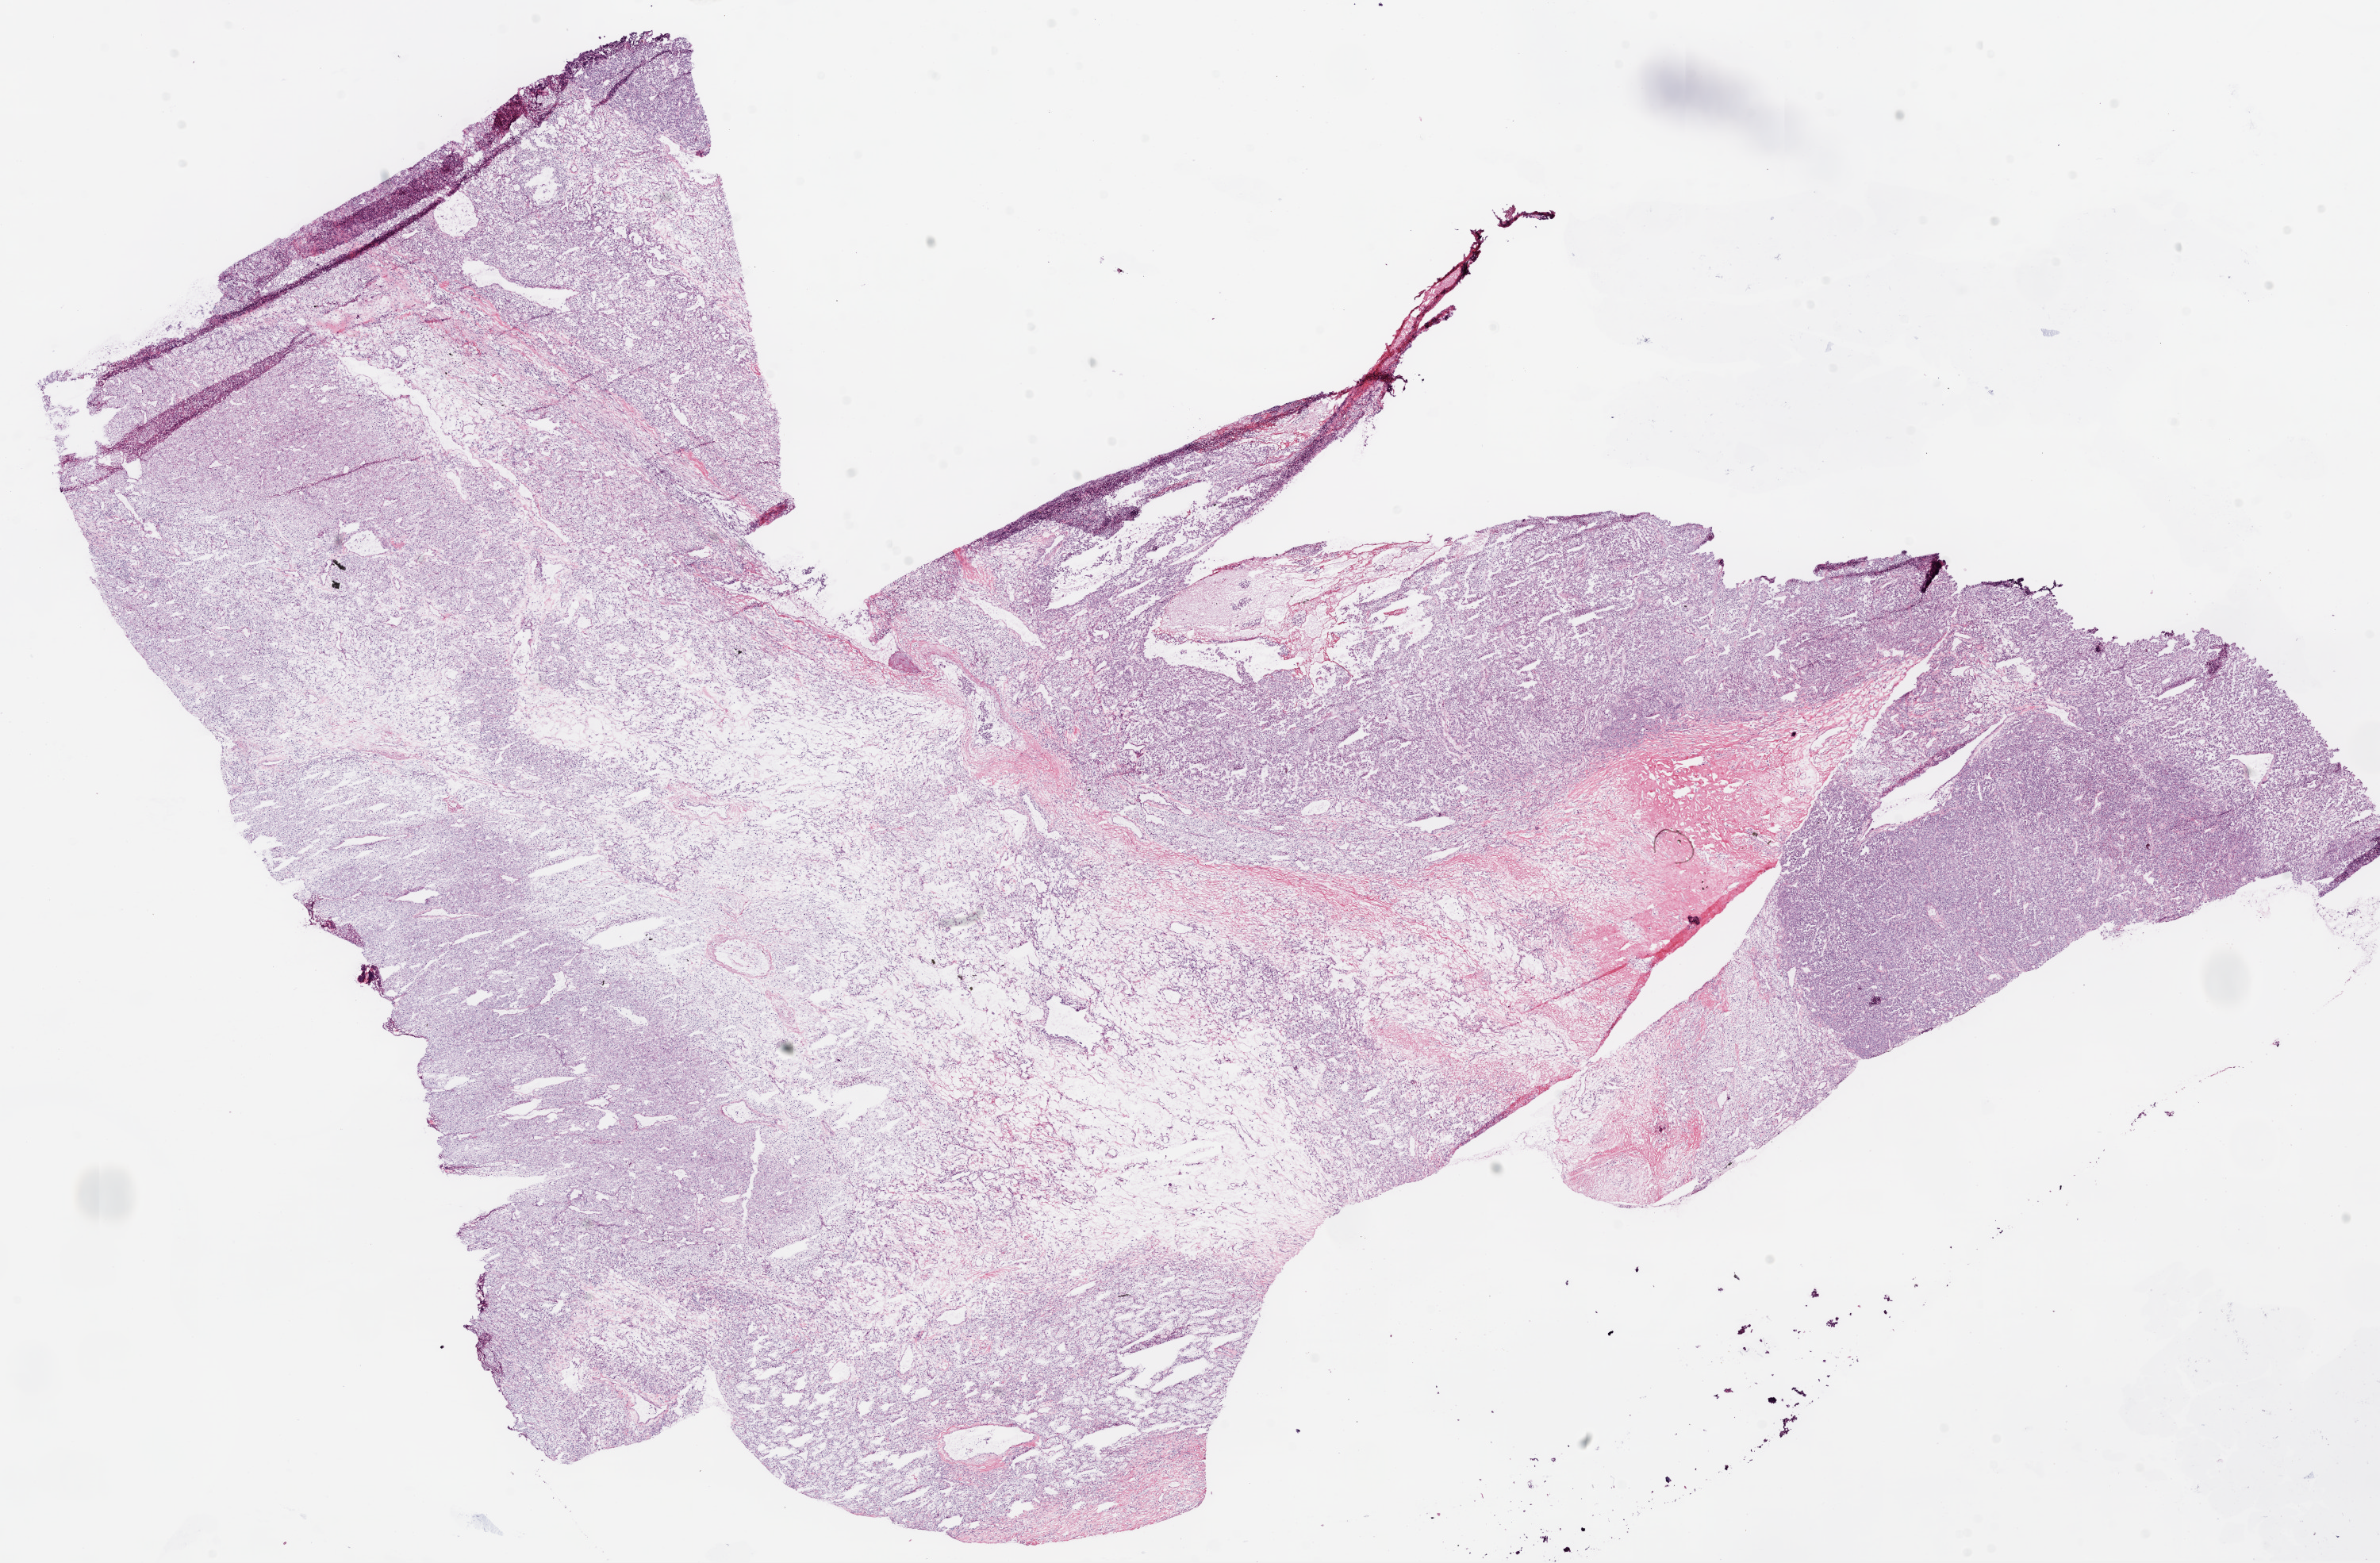
Digitized H&E-stained tissue section (whole slide), a low-resolution overview of the entire scanned area, about 24.1 x 15.8 mm. Frozen section from the bottom of the tissue portion. Sample: primary tumour, kidney. Female patient; age at initial diagnosis 53 years.
Histologic diagnosis: Clear cell adenocarcinoma, NOS.